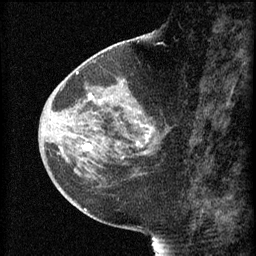
Breast MRI (dynamic contrast-enhanced), one sagittal slice. Position 27 of 60 along the scan axis. 3 images stored at this slice position (order not interpretable as contrast timing). 1.5 T. TE 4.2 ms, TR 8.2 ms. 2 mm slice thickness. 256 × 256 image matrix, field of view 180 × 180 mm. Patient: female, 44 years.
Outlined on this slice (semi-automatically segmented with operator editing):
- analysis volume of interest (the breast-tissue region the enhancement analysis was run in; not a lesion): box from (x=73, y=82) to (x=169, y=165) px
- tumour enhancement mask (voxels above the 70 % enhancement threshold inside the analysis volume of interest): (x=83, y=94)–(x=155, y=159)